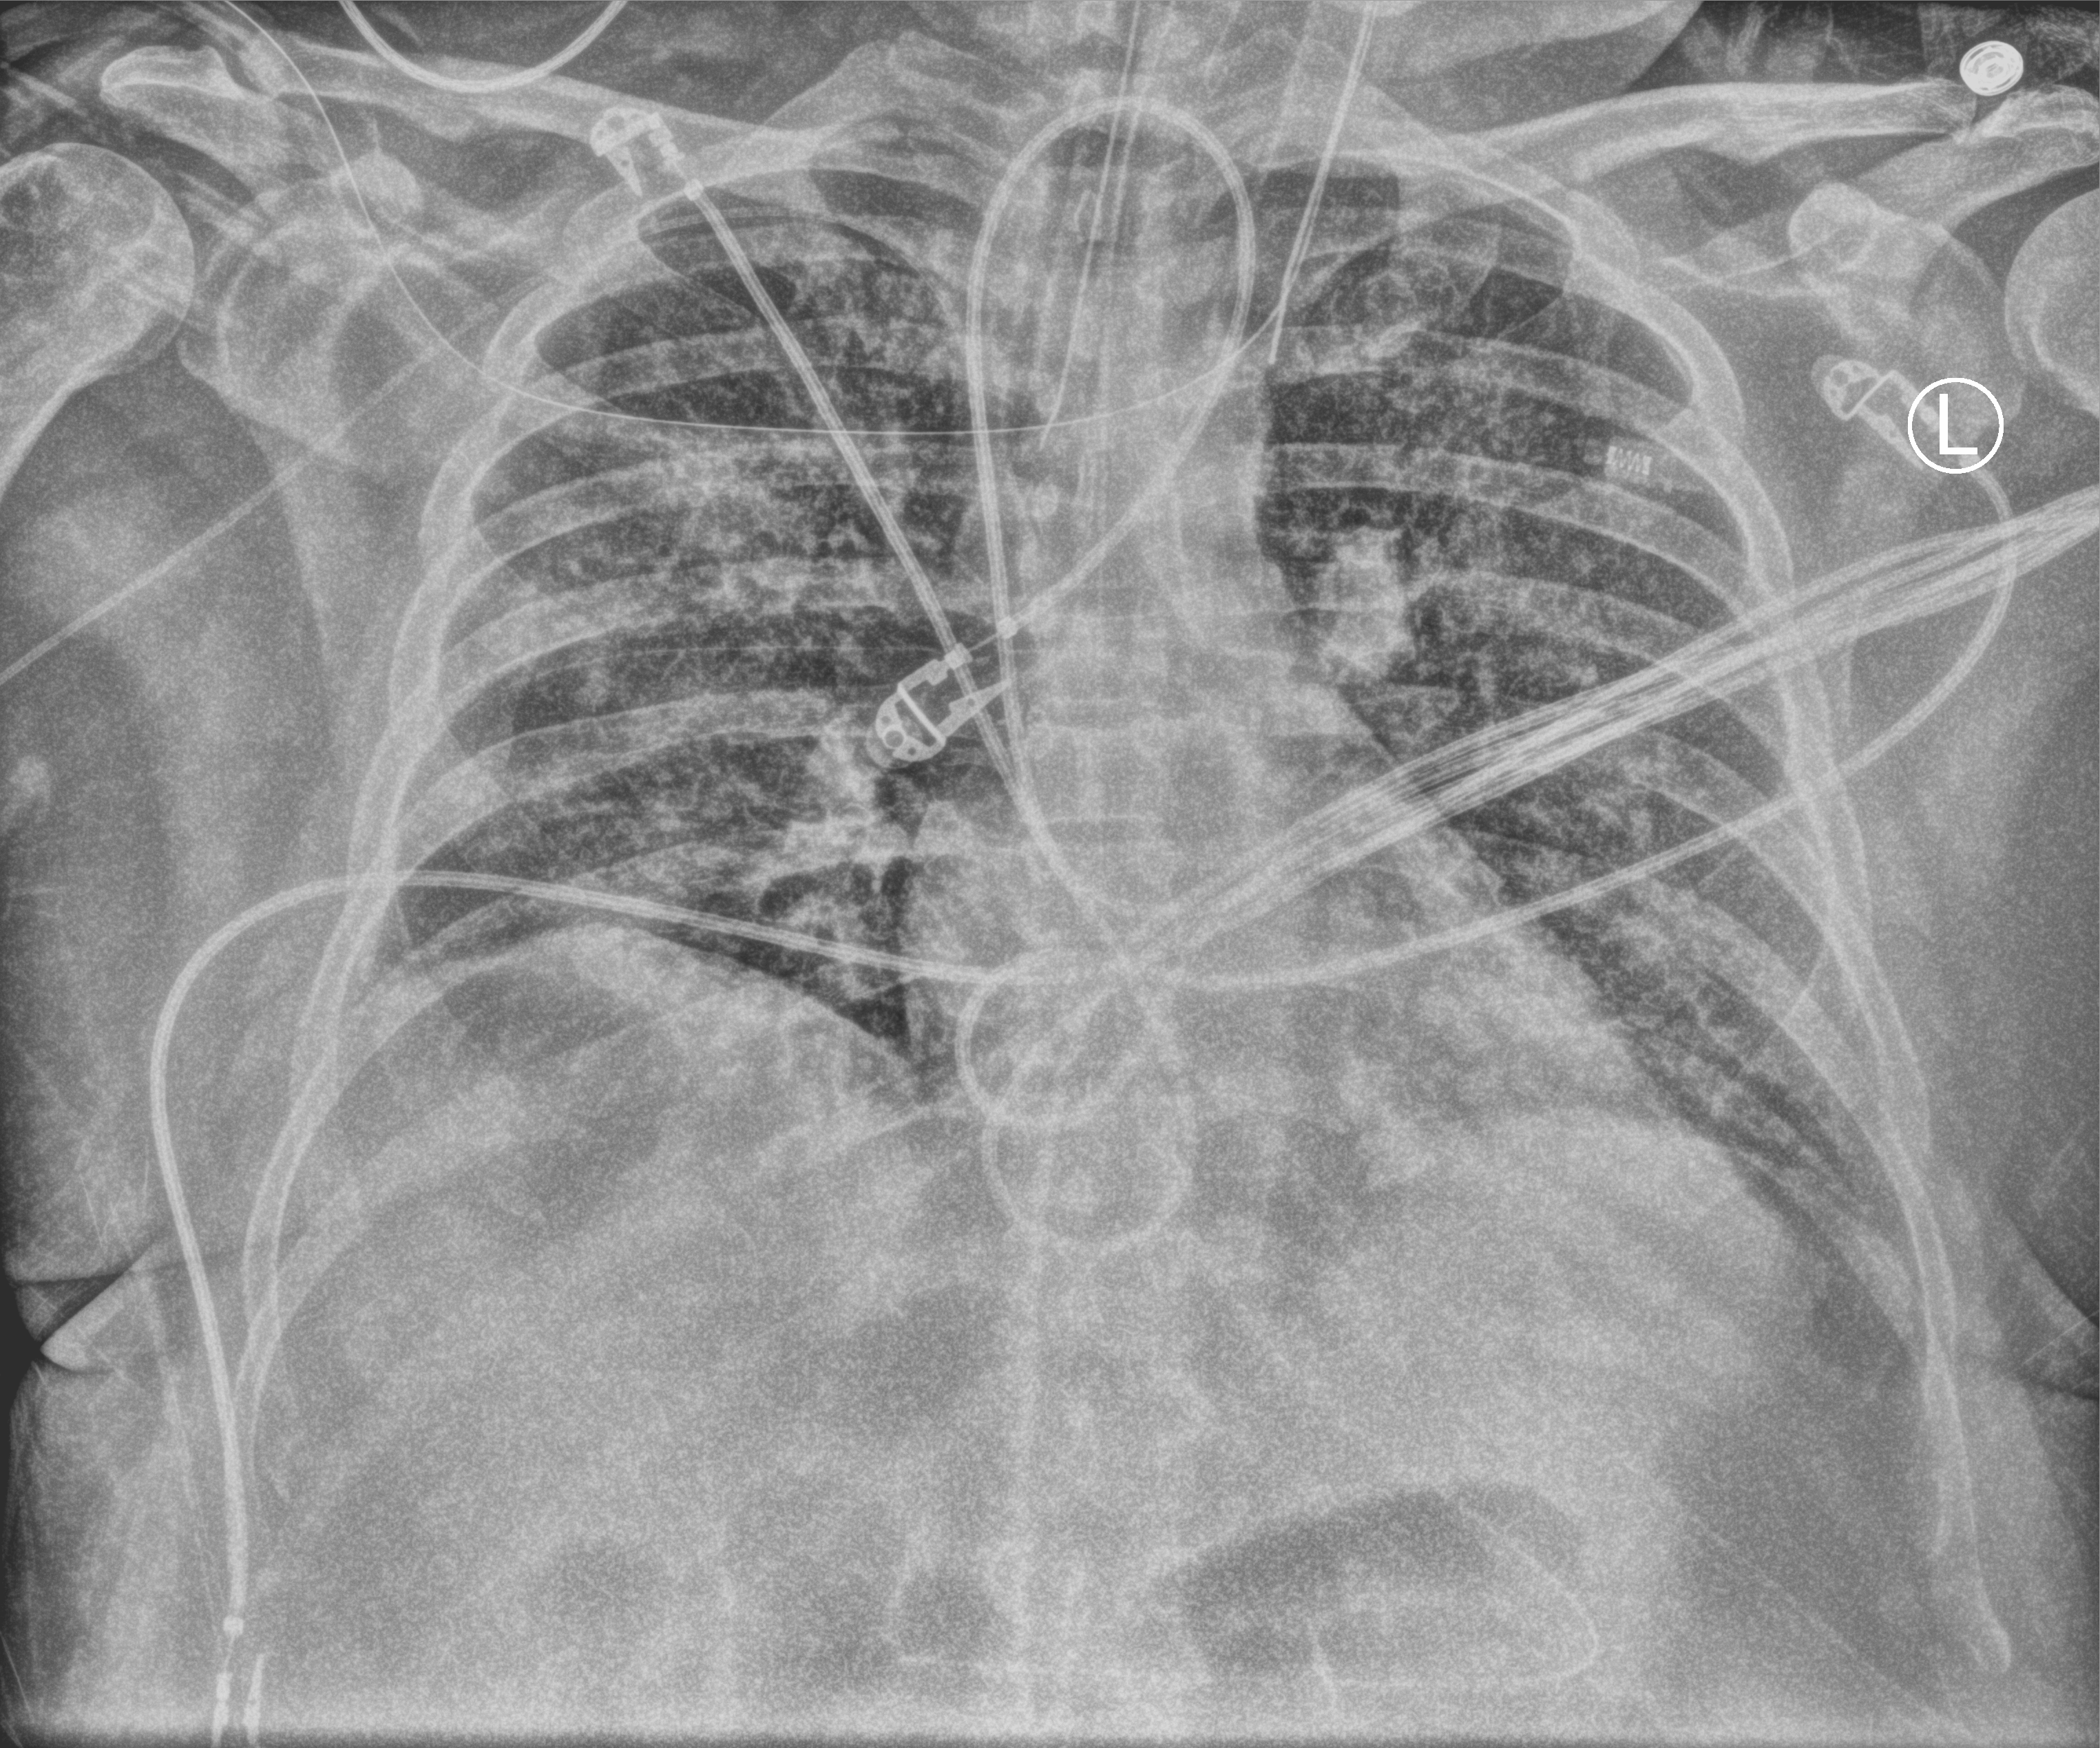
Portable chest radiograph, anteroposterior (AP) projection. Patient hospitalised with COVID-19; male, aged 18–59 years.
Admission-level facts for this patient (not findings on this image; timing relative to this image not recorded): mechanically ventilated during this hospital stay: yes; admitted to intensive care during this hospital stay: yes; smoking status (admission record): never.